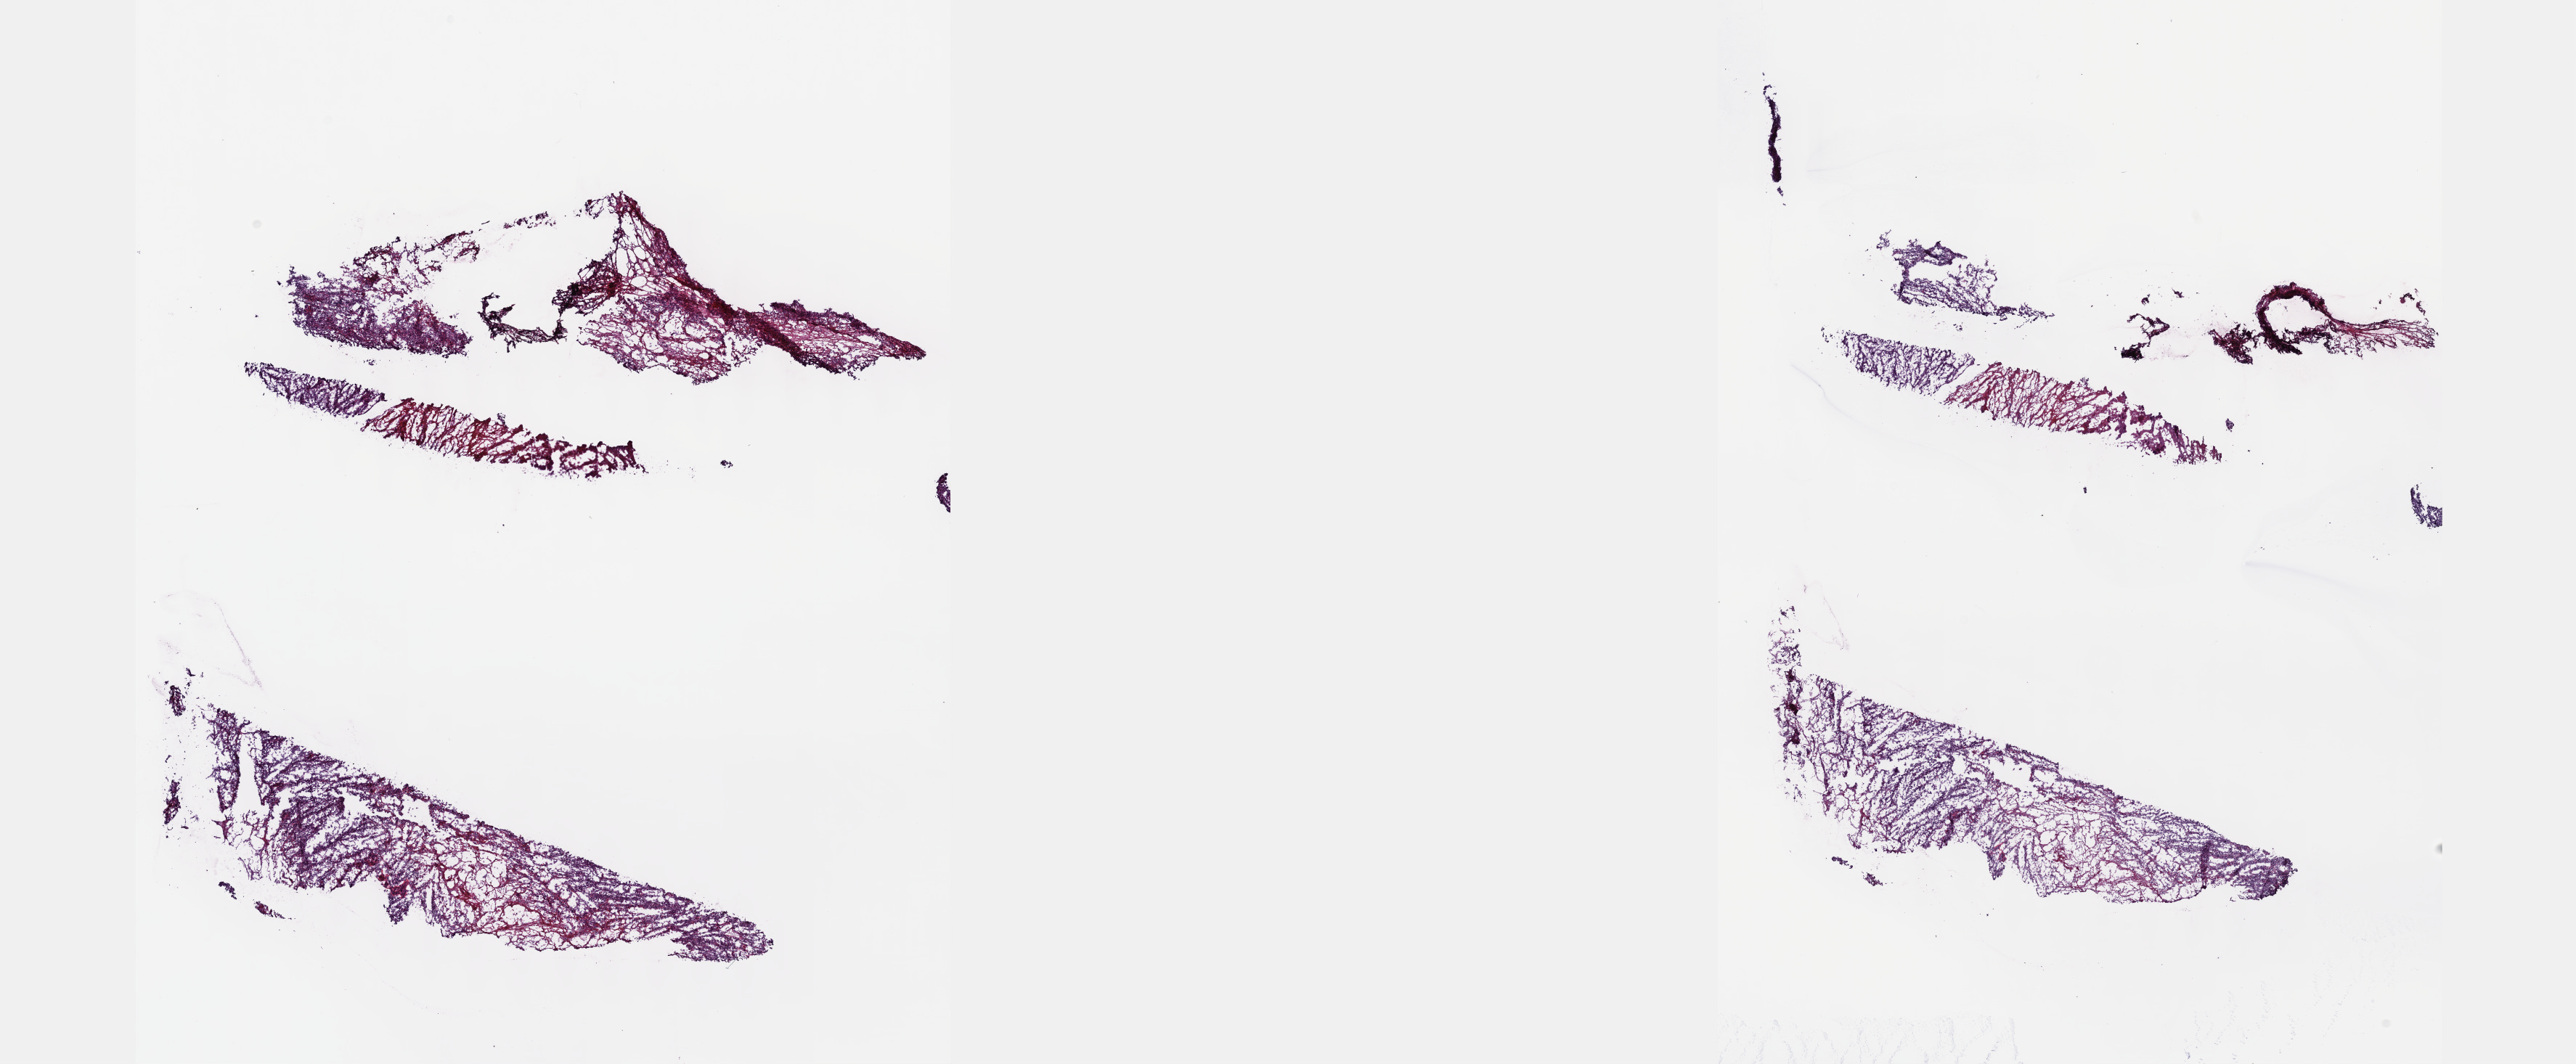
Whole-slide histology image, Hematoxylin and eosin (H&E) stained, whole scanned area (about 28.7 x 11.8 mm, slide scanned at 40x) shown as a low-resolution overview. Frozen section from the top of the tissue portion. Primary tumour sample from the connective, subcutaneous and other soft tissues. Patient: female, age at initial diagnosis 78 years. Composition of this section per pathologist review: tumour cells 75%, tumour nuclei 75%, normal cells 0%, stromal cells 23%, necrosis 2%. Infiltration values recorded for this section: lymphocyte infiltration 2%, monocyte infiltration 2%, neutrophil infiltration 2%.
• histologic diagnosis: Leiomyosarcoma, NOS